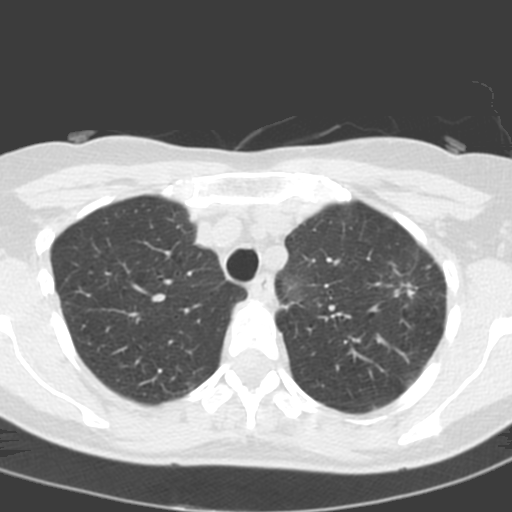
Low-dose screening chest CT, one axial slice. Position 152 of 193 along the scan axis. Lung window (W 1500 / L -600 HU). 512 × 512 image matrix, field of view 272 × 272 mm.
Outlined on this slice (expert manual segmentation):
- lesion 1 (tumor, upper lobe of left lung): box from (x=394, y=283) to (x=414, y=297) px